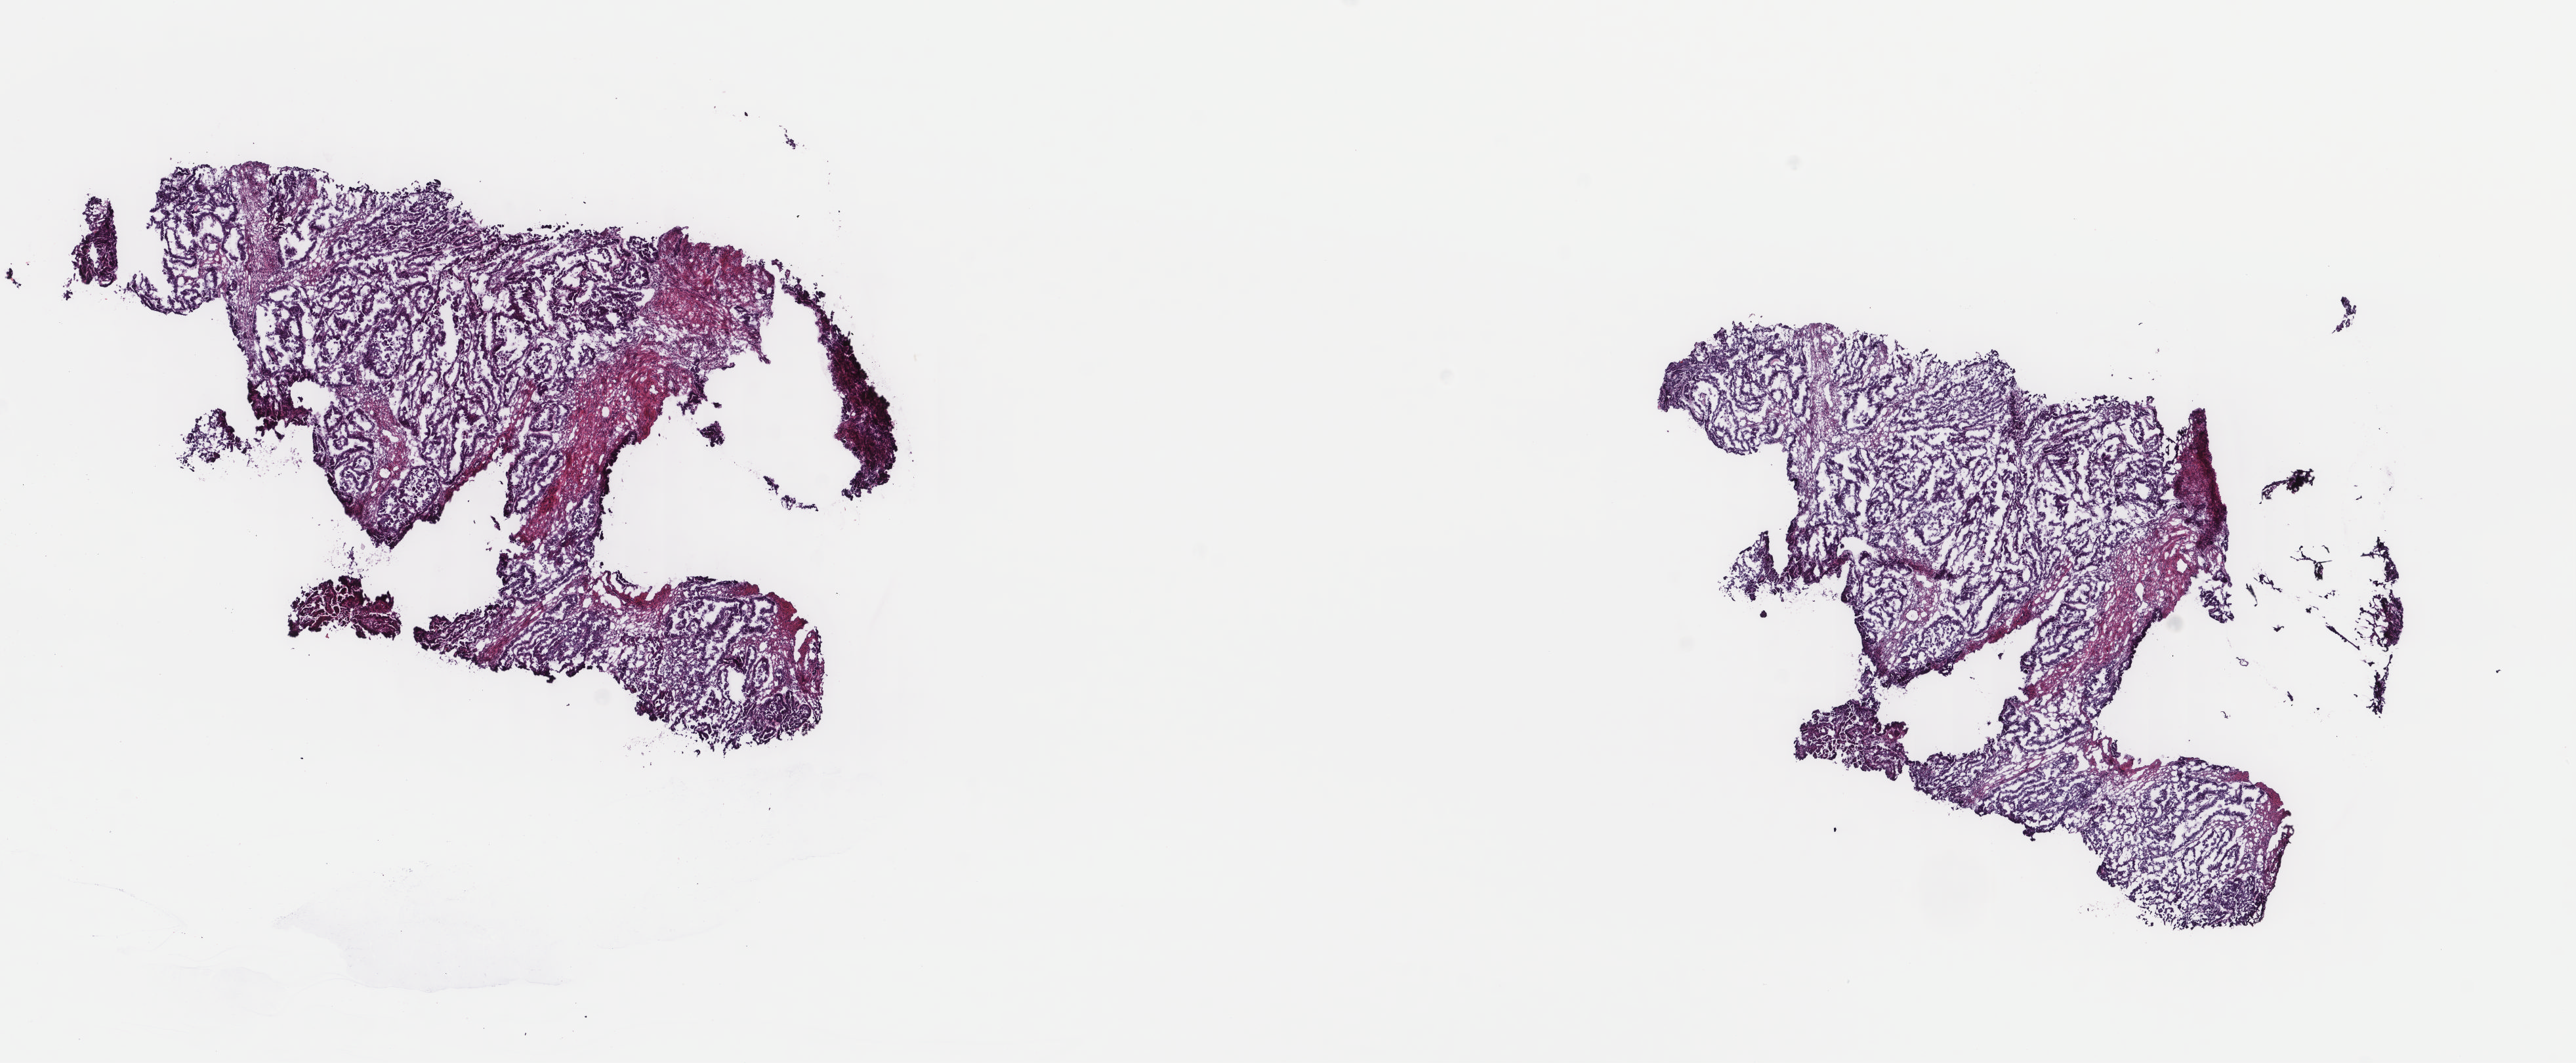
H&E-stained whole-slide image, shown as a low-resolution overview of the whole scanned area (about 15.6 x 6.4 mm, from a 40x scan), frozen section from the top of the tissue portion, uterus, primary tumour sample. Female patient; age at initial diagnosis 70 years. Histologic grade: high grade. Pathologist review of this section (percent, as recorded): tumour cells 57%, tumour nuclei 60%, normal cells 0%, stromal cells 40%, necrosis 3%. Infiltration values recorded for this section: lymphocyte infiltration 3%, monocyte infiltration 4%, neutrophil infiltration 1%.
FIGO stage: IIIC. Diagnosis: Serous cystadenocarcinoma, NOS (endometrium).